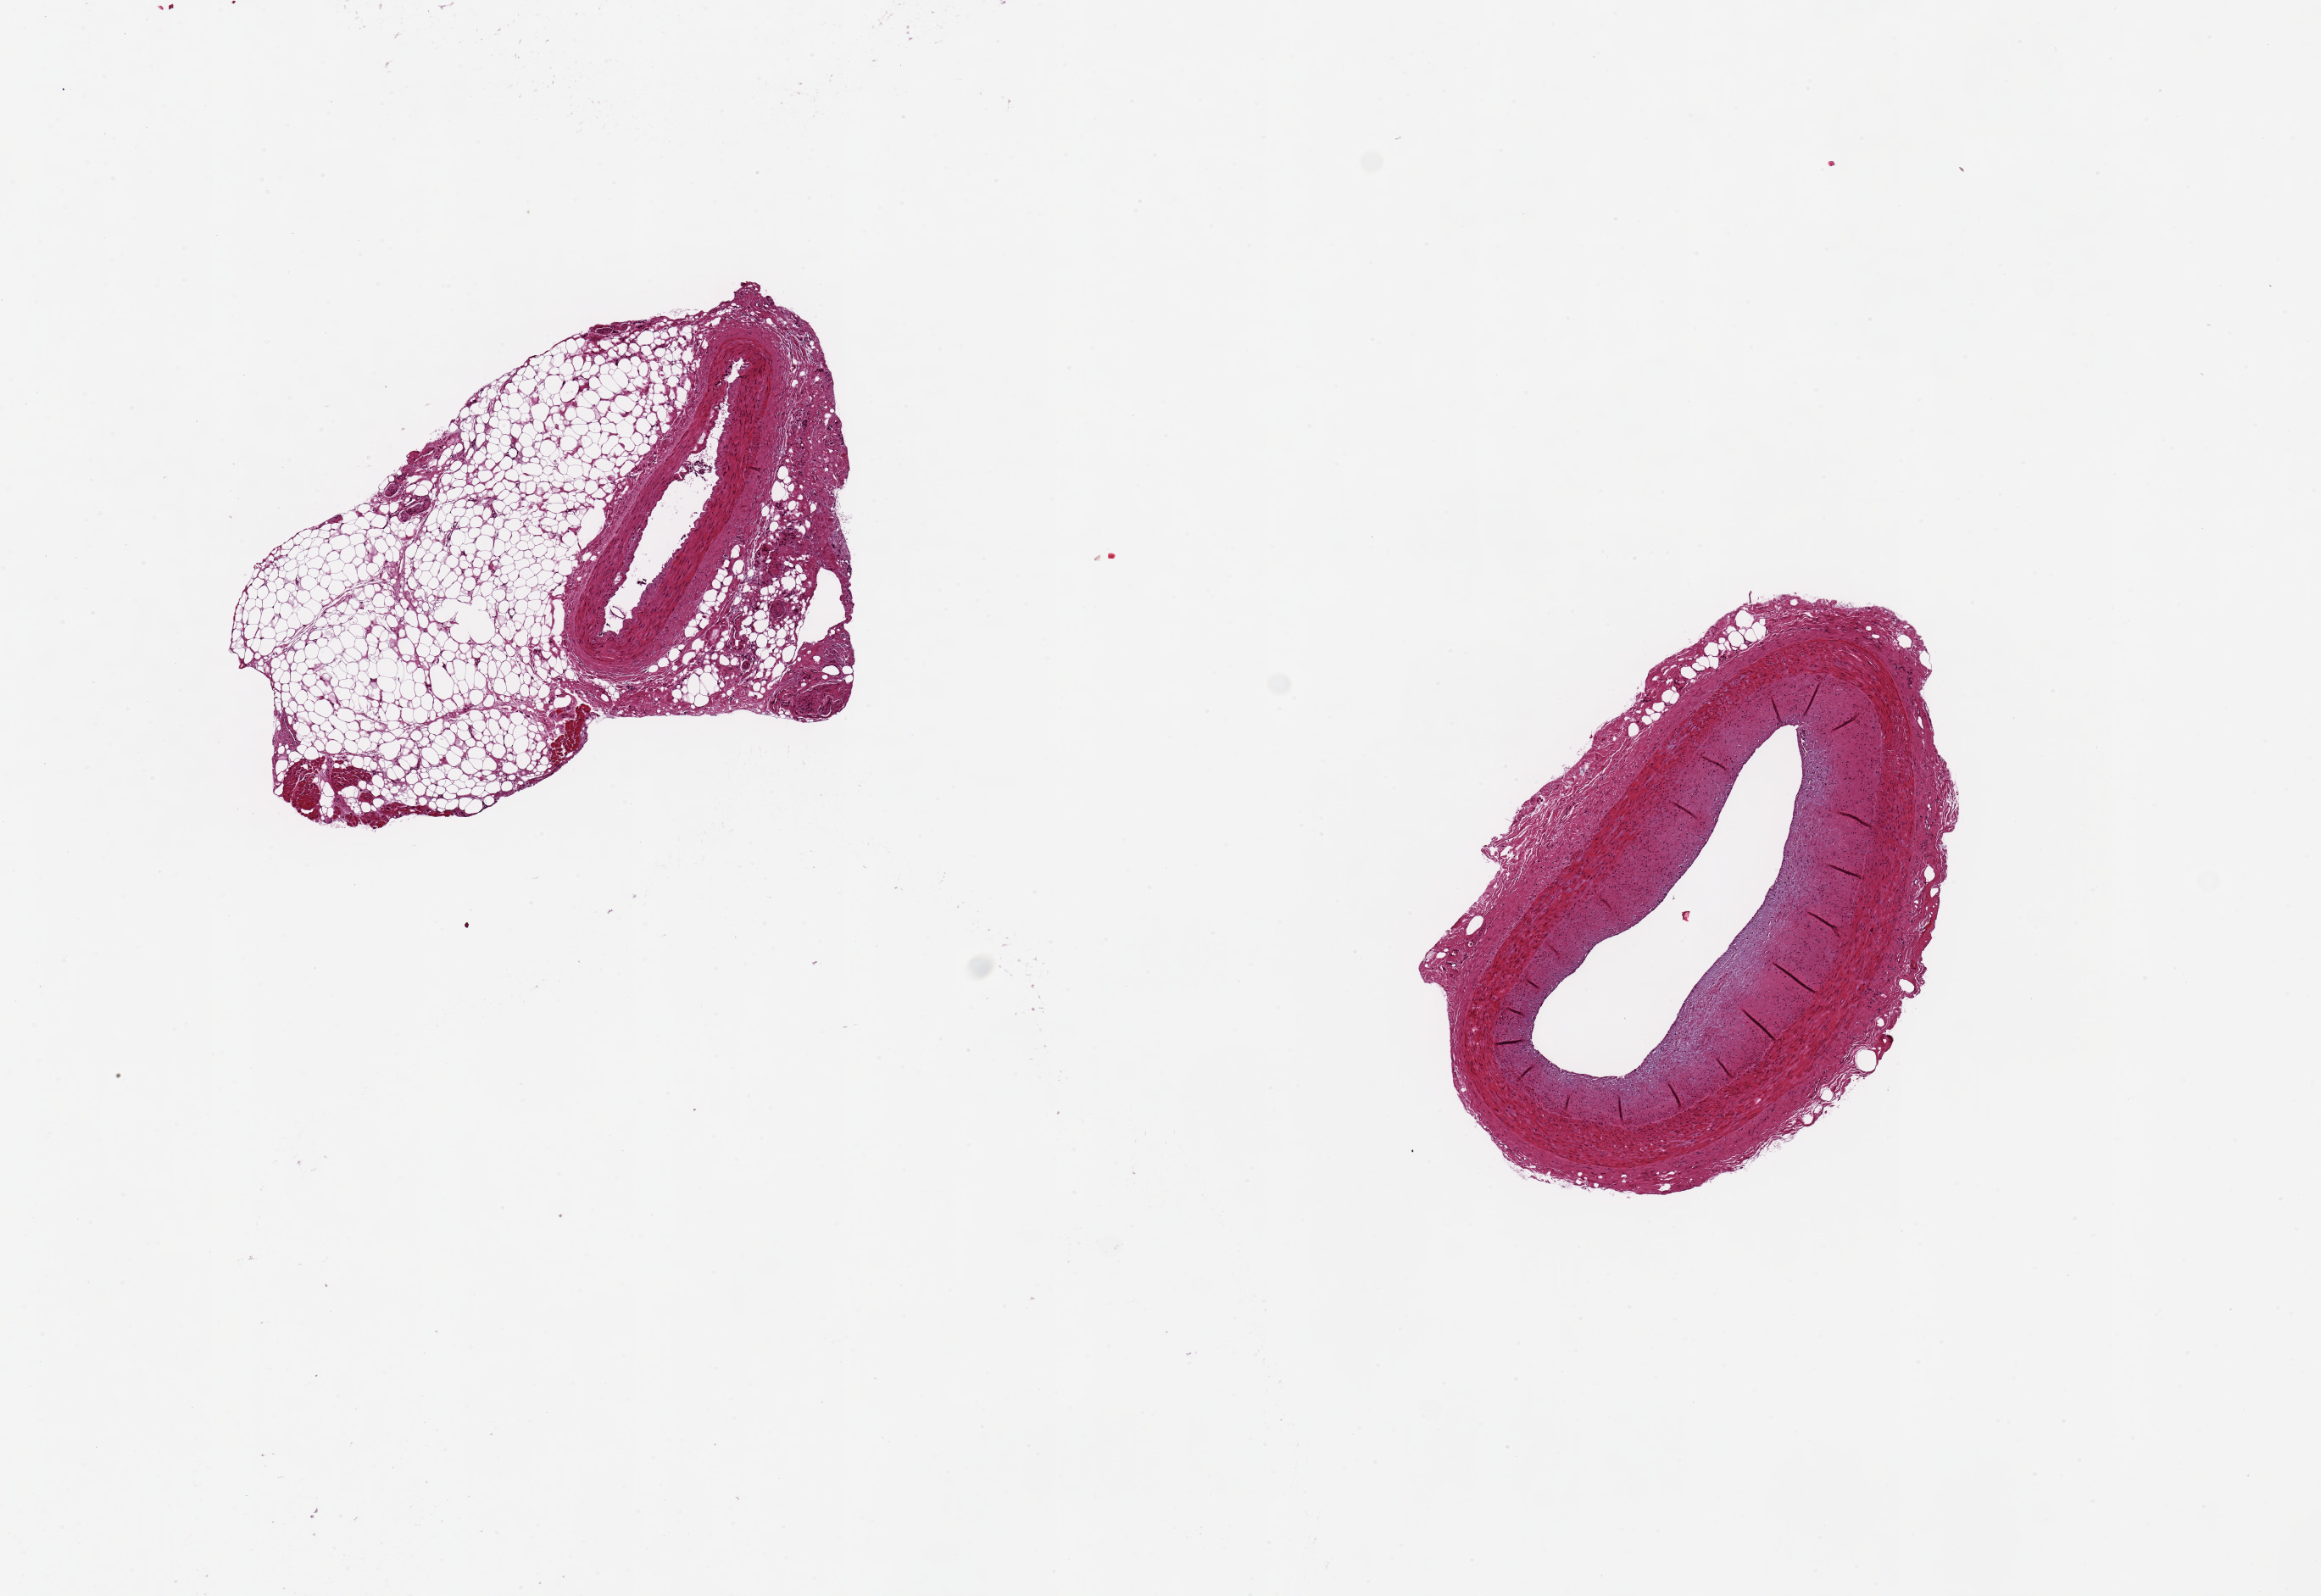
H&E whole-slide image, brightfield — low-resolution overview of the scanned area, about 10.8 x 7.4 mm (slide scanned at 20x), PAXgene-fixed paraffin-embedded (PFPE) section, target tissue: coronary artery, tissue donor sample. Male donor.
Reviewer comment on this tissue sample: 2 aliquots, one ~3x2mm, clean, one ~1.6x0.5mm embedded in 3x2mm adipose tissue. See comment below.